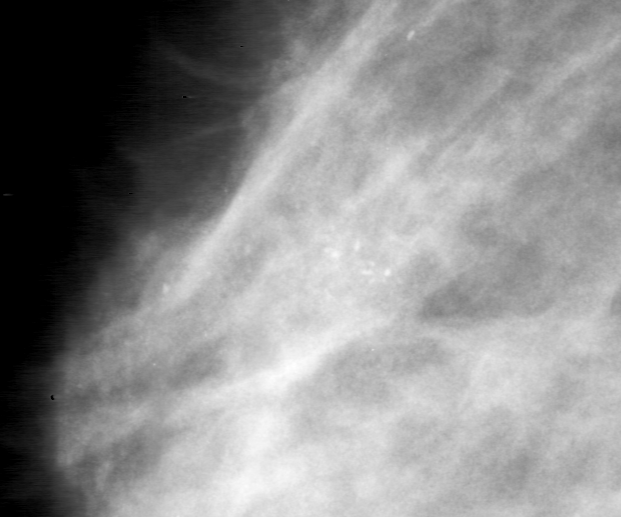
Crop from a digitized film mammogram around one marked abnormality; right breast; MLO view.
Marked abnormality: calcifications, morphology pleomorphic, distribution clustered; BI-RADS assessment category 0 (incomplete: needs additional imaging); pathology (as recorded): malignant.